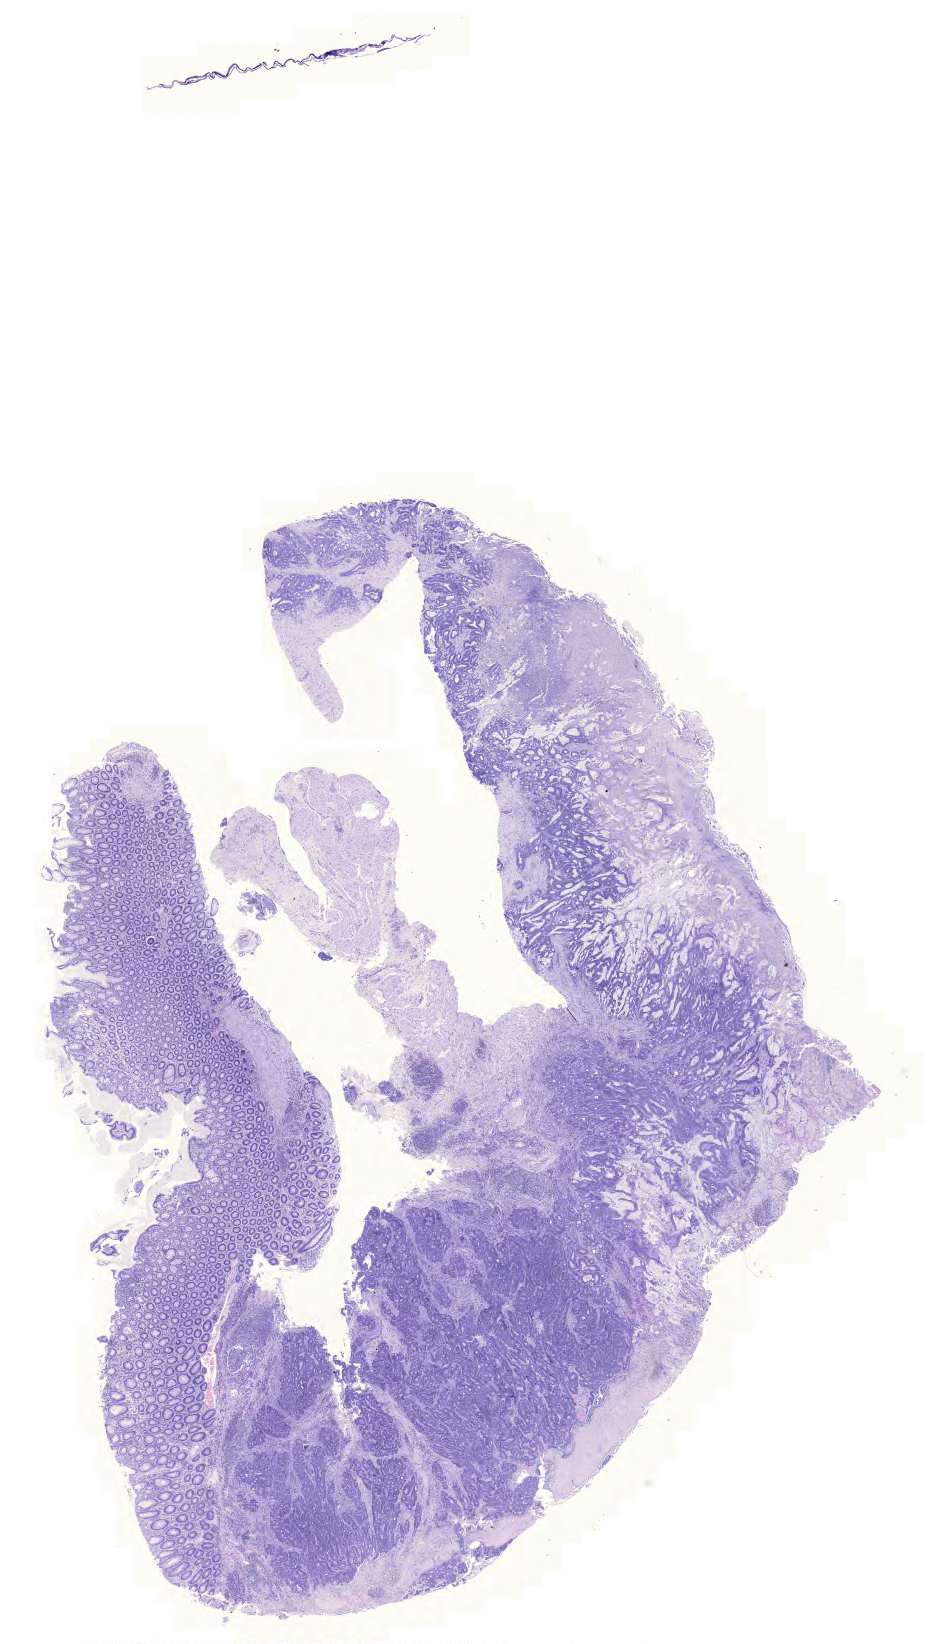
Whole-slide histology image, Hematoxylin and eosin (H&E) stained, whole scanned area (about 14.1 x 24.5 mm, slide scanned at 20x) shown as a low-resolution overview. Formalin-fixed paraffin-embedded (FFPE) diagnostic section. Sample: primary tumour, colon. Female, age 60 years at initial diagnosis.
Pathologic diagnosis: Mucinous adenocarcinoma.